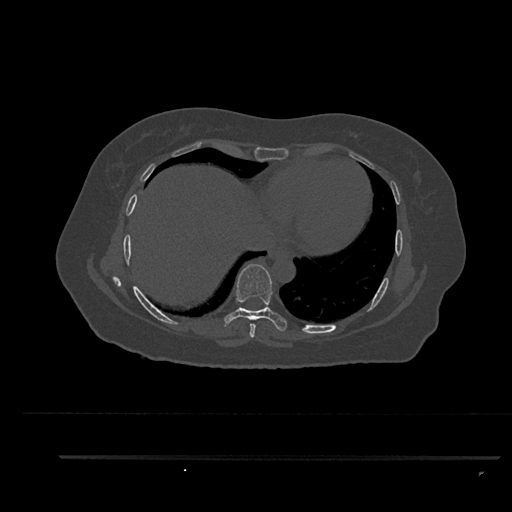
CT including the spine, one axial slice; position 465 of 797 along the scan axis; reconstruction kernel Br40s/3; 120 kVp; bone window (W 1800 / L 400 HU); 512 × 512 image matrix. Female patient, age 44 years. From the clinical record (not read from this slice): primary cancer: renal; vertebrae with lytic lesions (as recorded): L1.
Outlined on this slice (semi-automatic segmentation, software-assisted and operator-edited):
- T7 vertebra: bounding box [x1, y1, x2, y2] px = [249, 323, 256, 338]
- T8 vertebra: [224, 264, 287, 331]